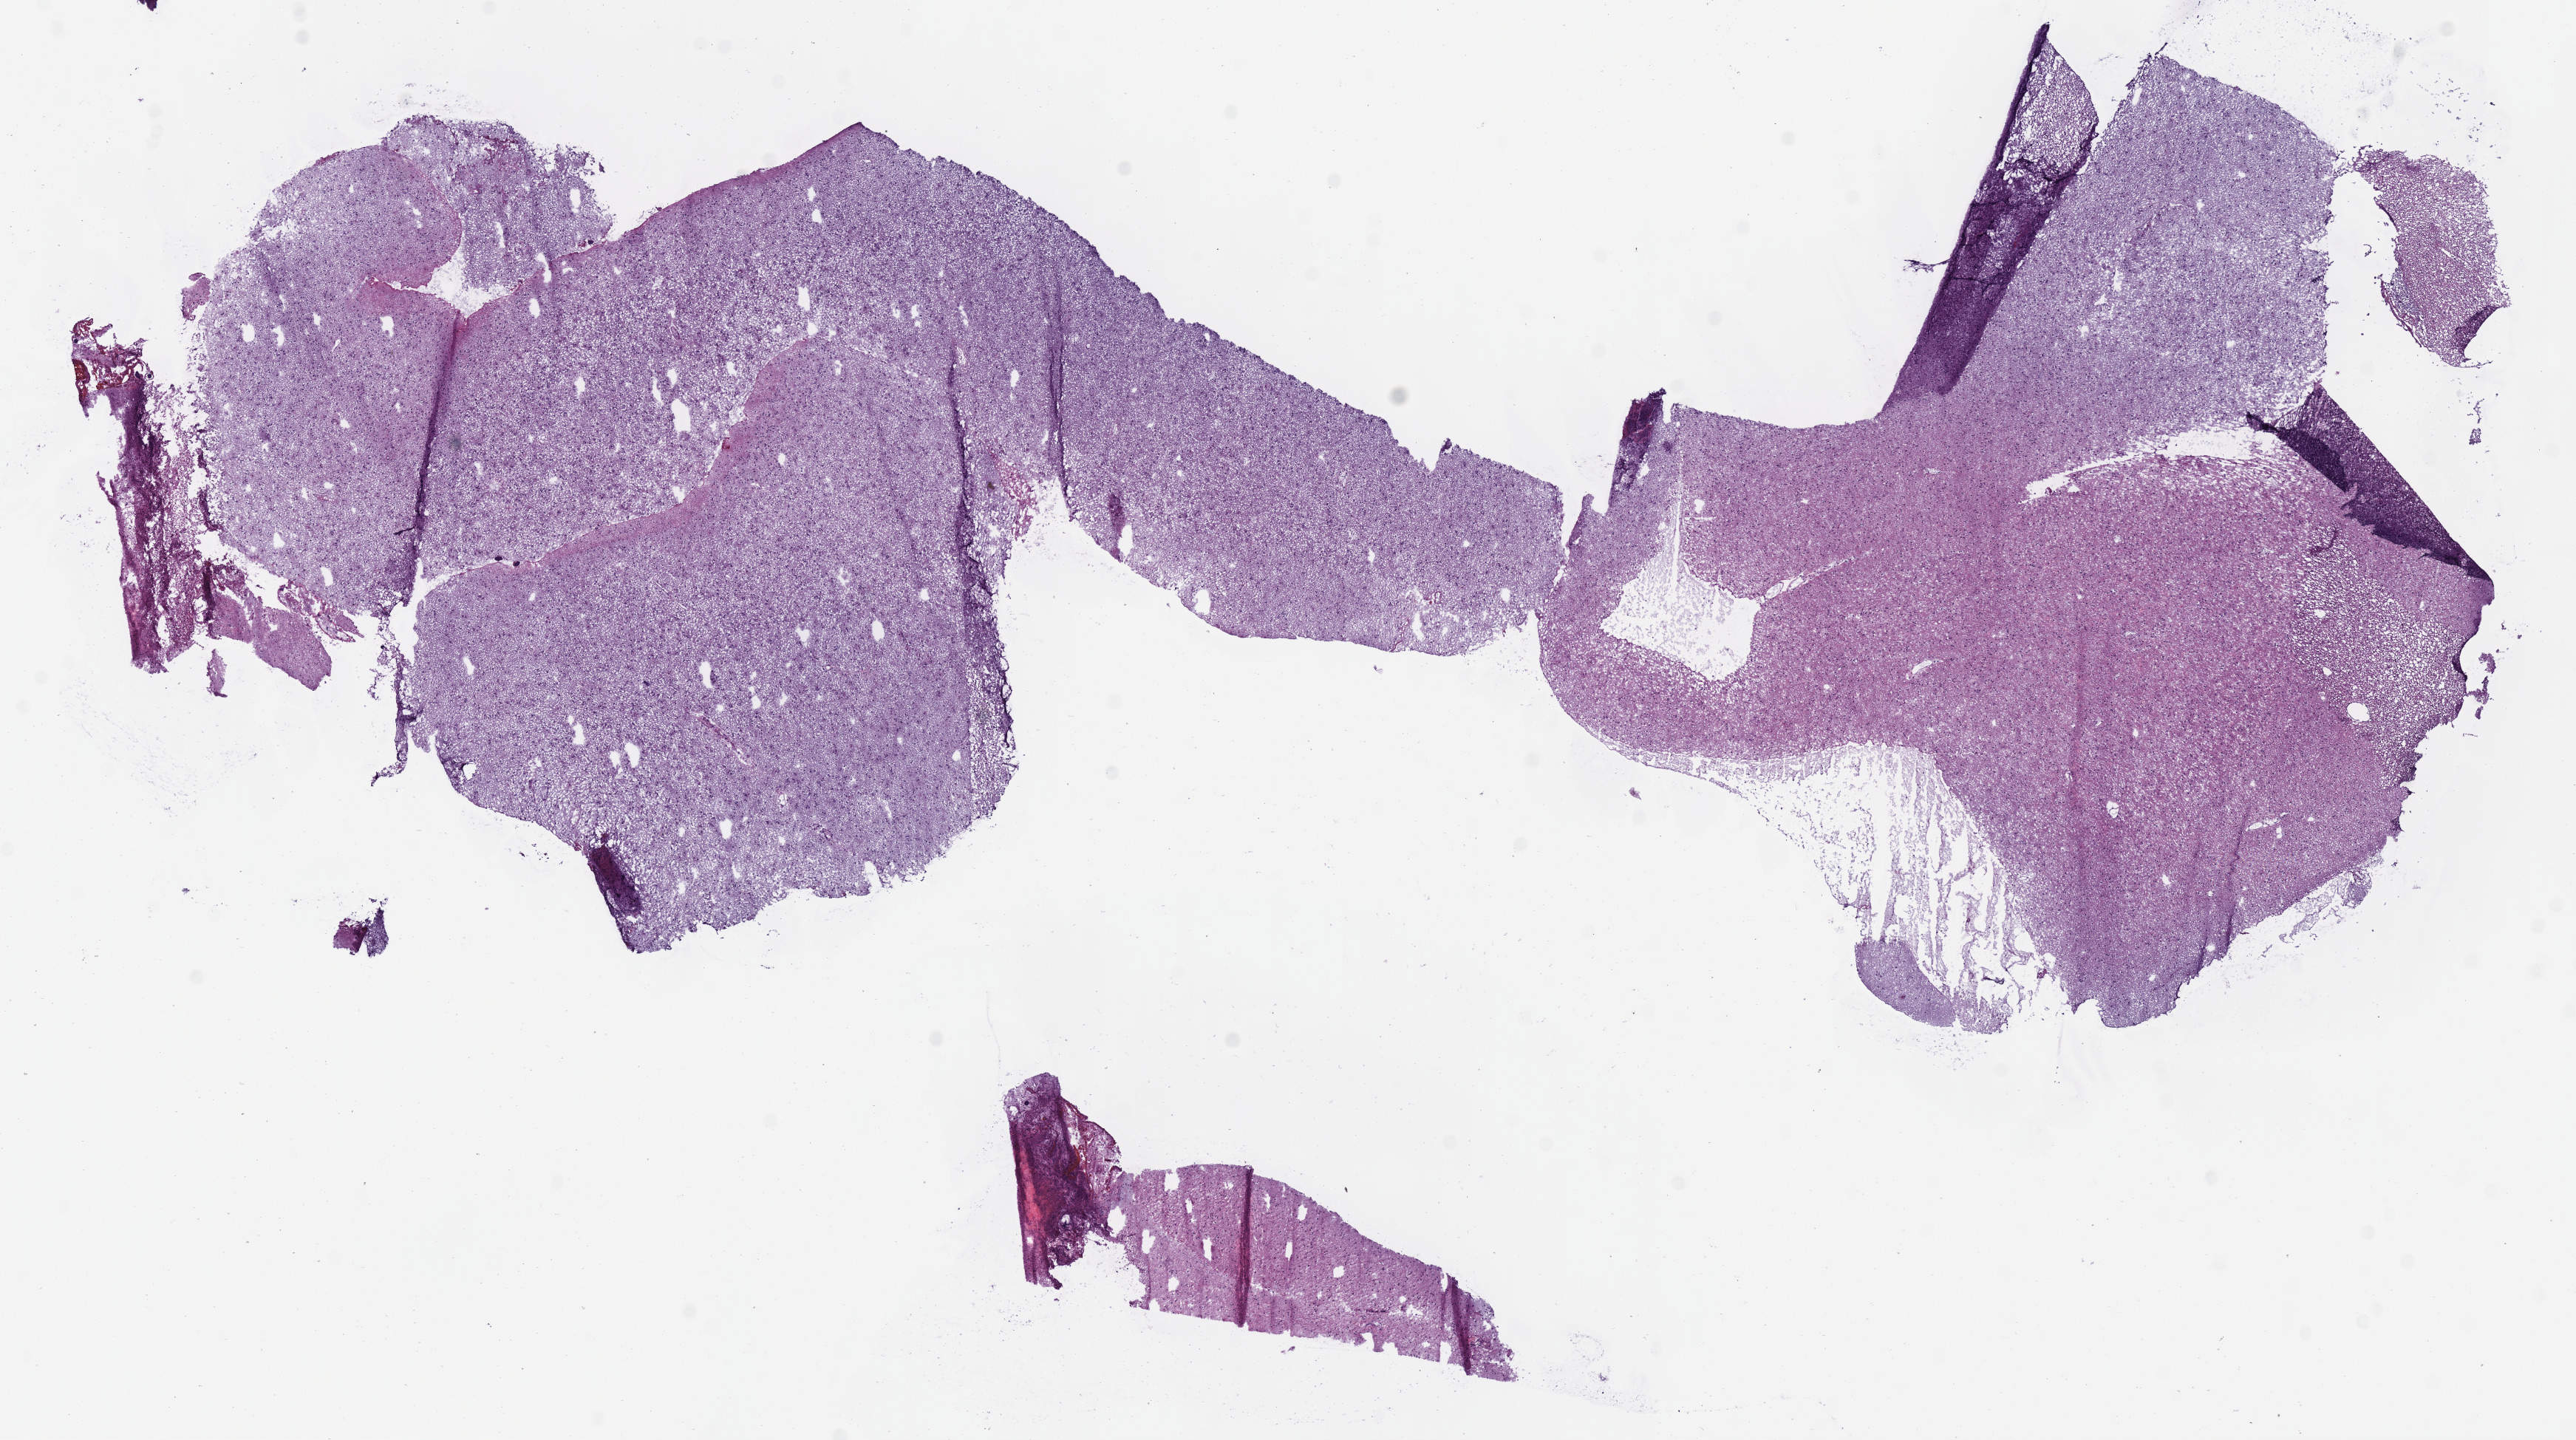
Hematoxylin and eosin (H&E) stained whole-slide image — low-resolution overview of the scanned area, about 13.7 x 7.7 mm (slide scanned at 40x), frozen section from the bottom of the tissue portion, sample: primary tumour, brain. Female patient; age at initial diagnosis 64 years. Histologic grade: G2 (moderately differentiated). Pathologist review of this section (percent, as recorded): tumour cells 100%, tumour nuclei 65%, normal cells 0%, stromal cells 0%, necrosis 0%.
Laterality: right. Pathologic diagnosis: Oligodendroglioma, NOS (cerebrum).